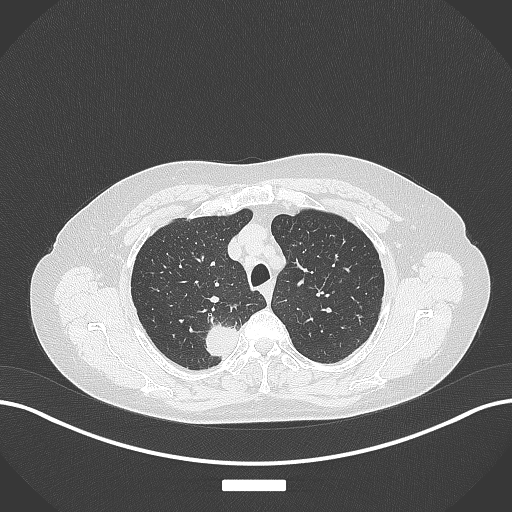
Chest CT, one axial slice. Position 311 of 357 along the scan axis. Reconstruction kernel B70f. Lung window (W 1500 / L -600 HU). 1 mm slice thickness. 512 × 512 image matrix, field of view 400 × 400 mm. Female patient, age 62 years. Case-level facts recorded for this patient, not image findings: clinical TNM (as recorded): T1c N1 M0.
Outlined on this slice (rectangle marked by the reading radiologist):
- lung tumour (recorded histology: squamous cell carcinoma): bounding box (x1, y1, x2, y2) in pixels: (204, 319, 240, 363)